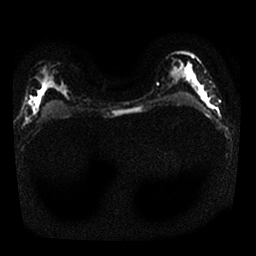
Breast MRI, one axial slice; slice 13 of 25 in the series (ordered by position); diffusion-weighted series; image 2 of 4 stored at this slice position (different b-values; order by instance number); 1.5 T; 256 × 256 image matrix, field of view 320 × 320 mm. Female patient.
Structures marked on this image (manually delineated by an expert):
- tumour on diffusion-weighted imaging: box from (x=191, y=77) to (x=207, y=101) px